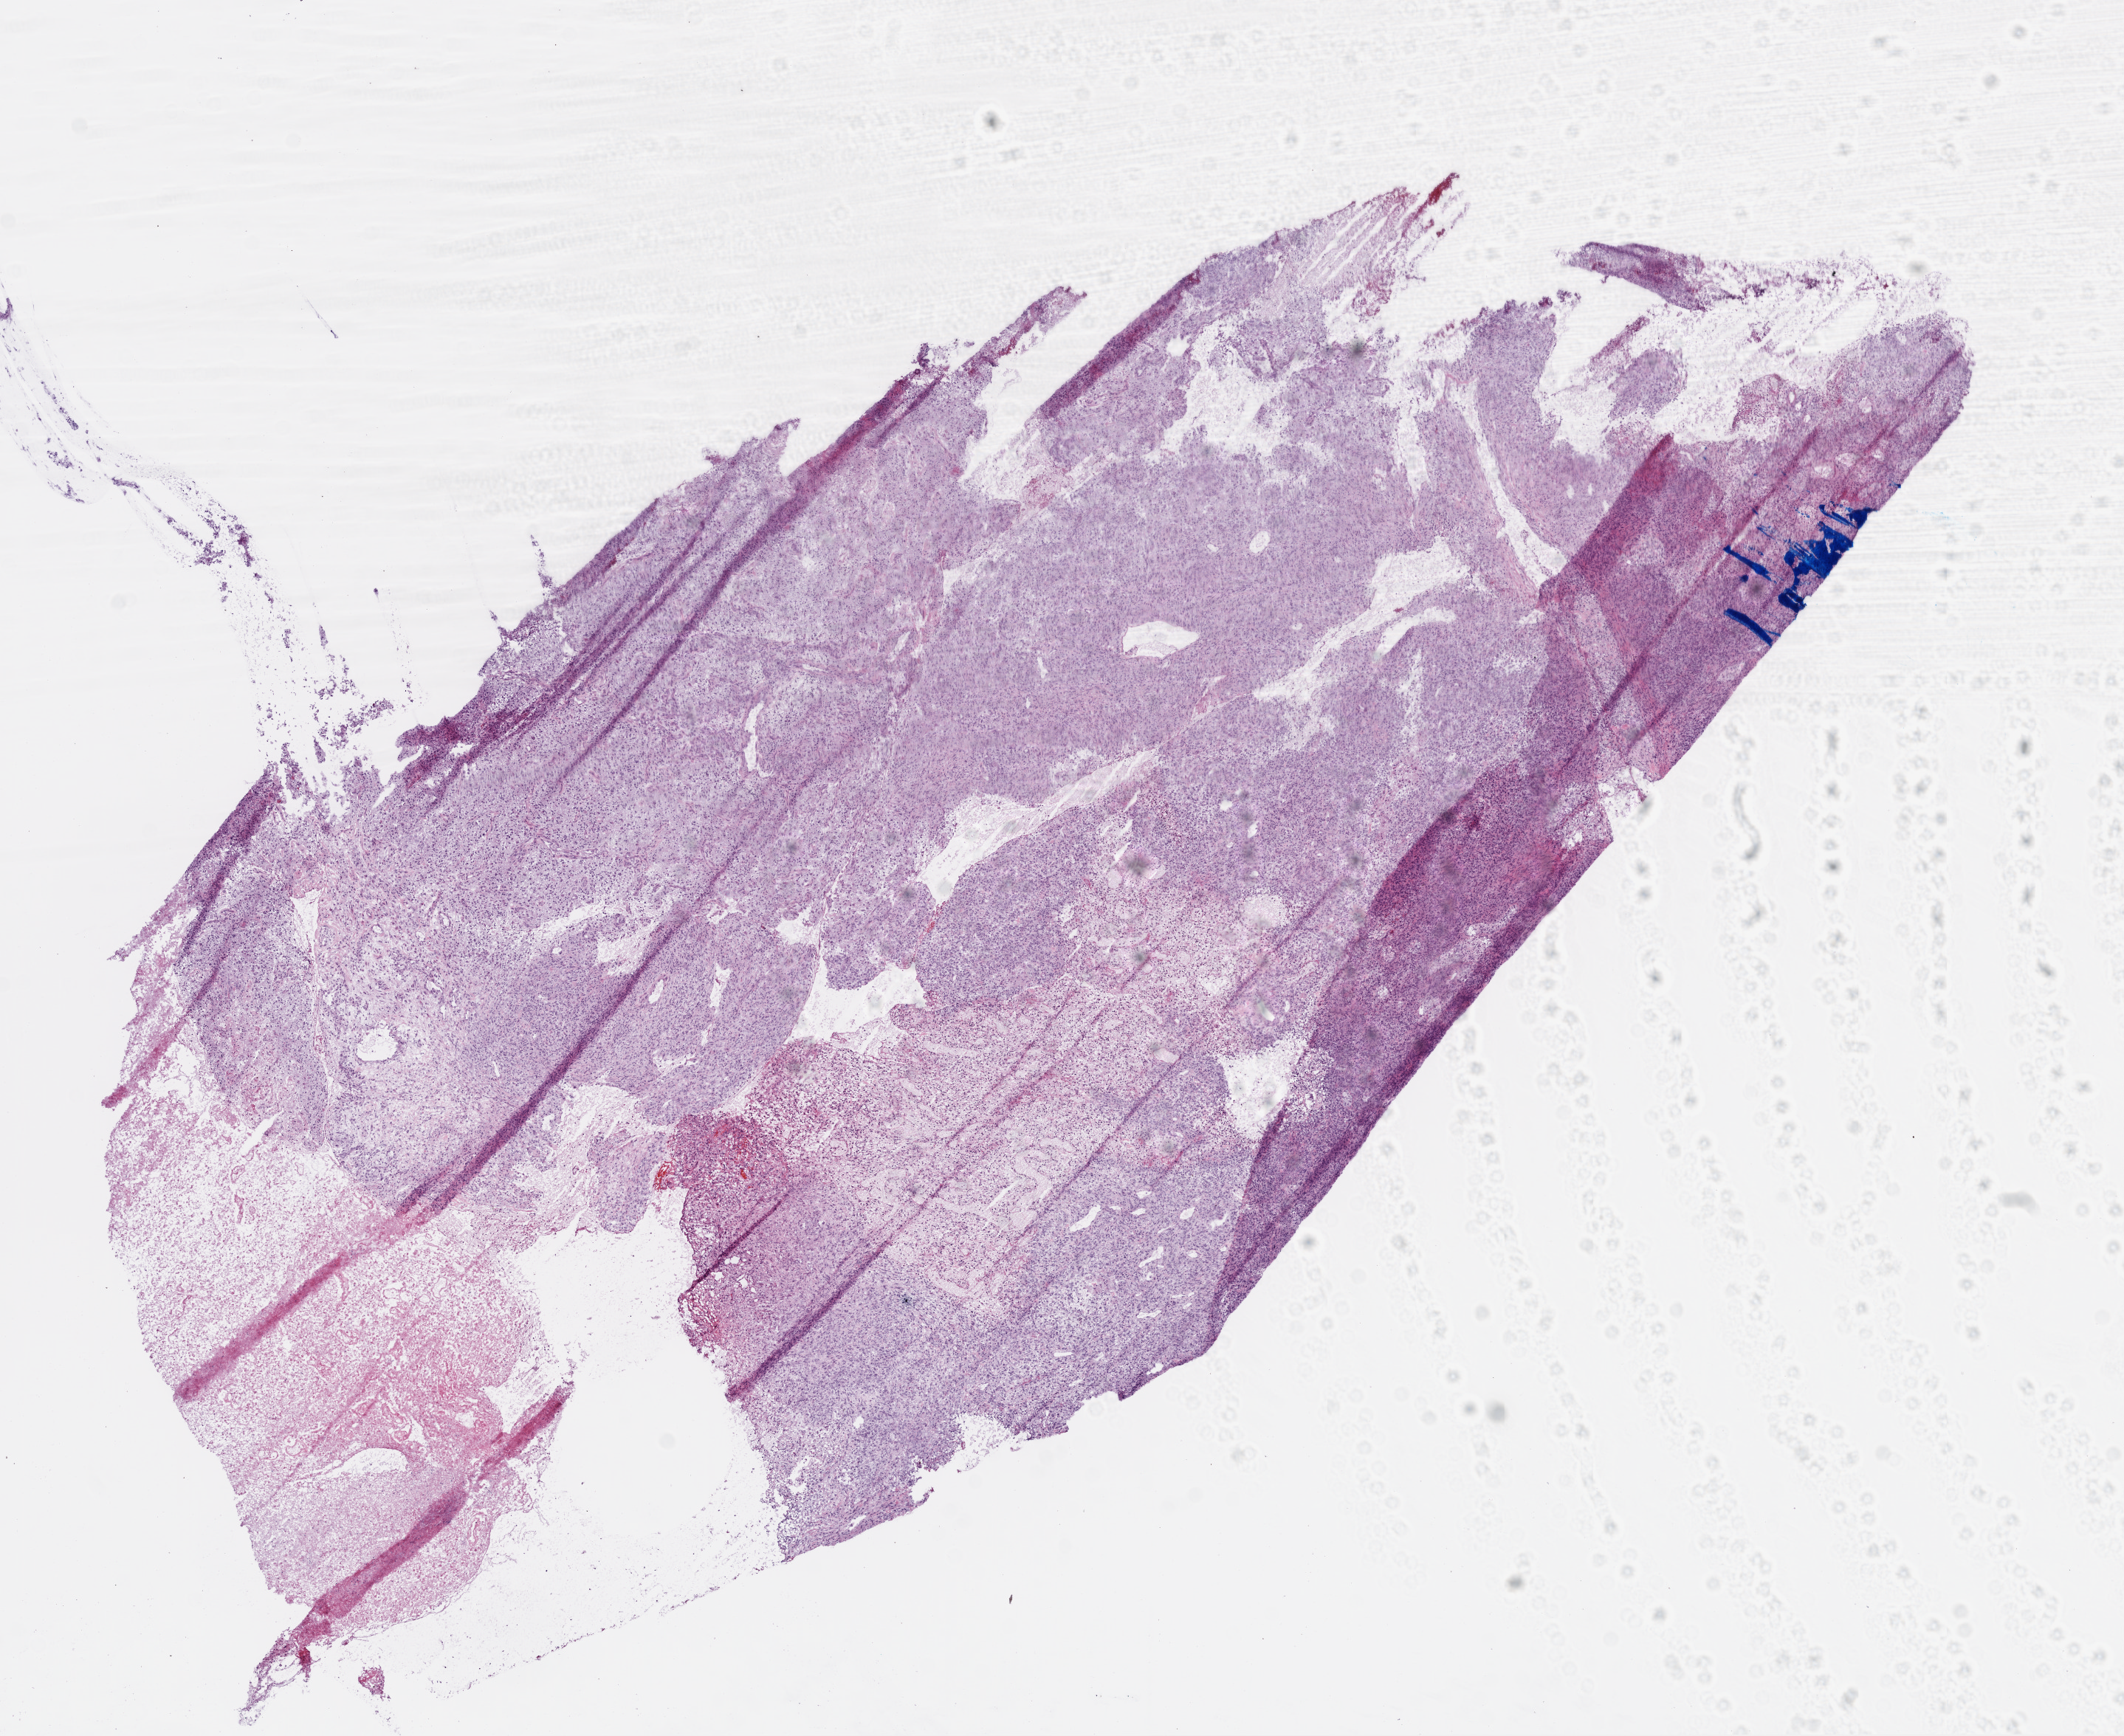
Hematoxylin and eosin (H&E) stained whole-slide image, shown as a low-resolution overview of the whole scanned area (about 11.6 x 9.5 mm, acquisition: 20x scan). Frozen section from the top of the tissue portion. Primary tumour sample from the brain. Male patient; age at initial diagnosis 61 years. Composition of this section per pathologist review: tumour cells 80%, tumour nuclei 95%, stromal cells 10%, necrosis 10%.
* diagnosis: Glioblastoma